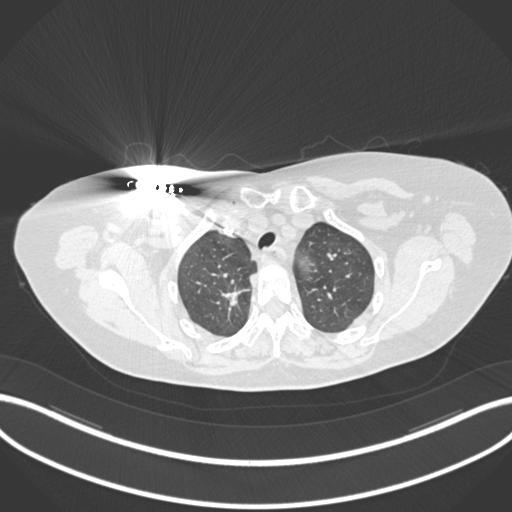
Chest CT, one axial slice. Slice 148 of 176 in the series (ordered by position). Reconstruction kernel B30f. 120 kVp. Lung window (W 1500 / L -600 HU). 1 mm slice thickness. 512 × 512 image matrix, field of view 400 × 400 mm. Patient: female, 72 years. From the clinical record (not read from this slice): clinical TNM (as recorded): T1c N0 M0.
Structures marked on this image (rectangle marked by the reading radiologist):
- lung tumour (recorded histology: adenocarcinoma): bounding box [x1, y1, x2, y2] px = [215, 284, 249, 313]